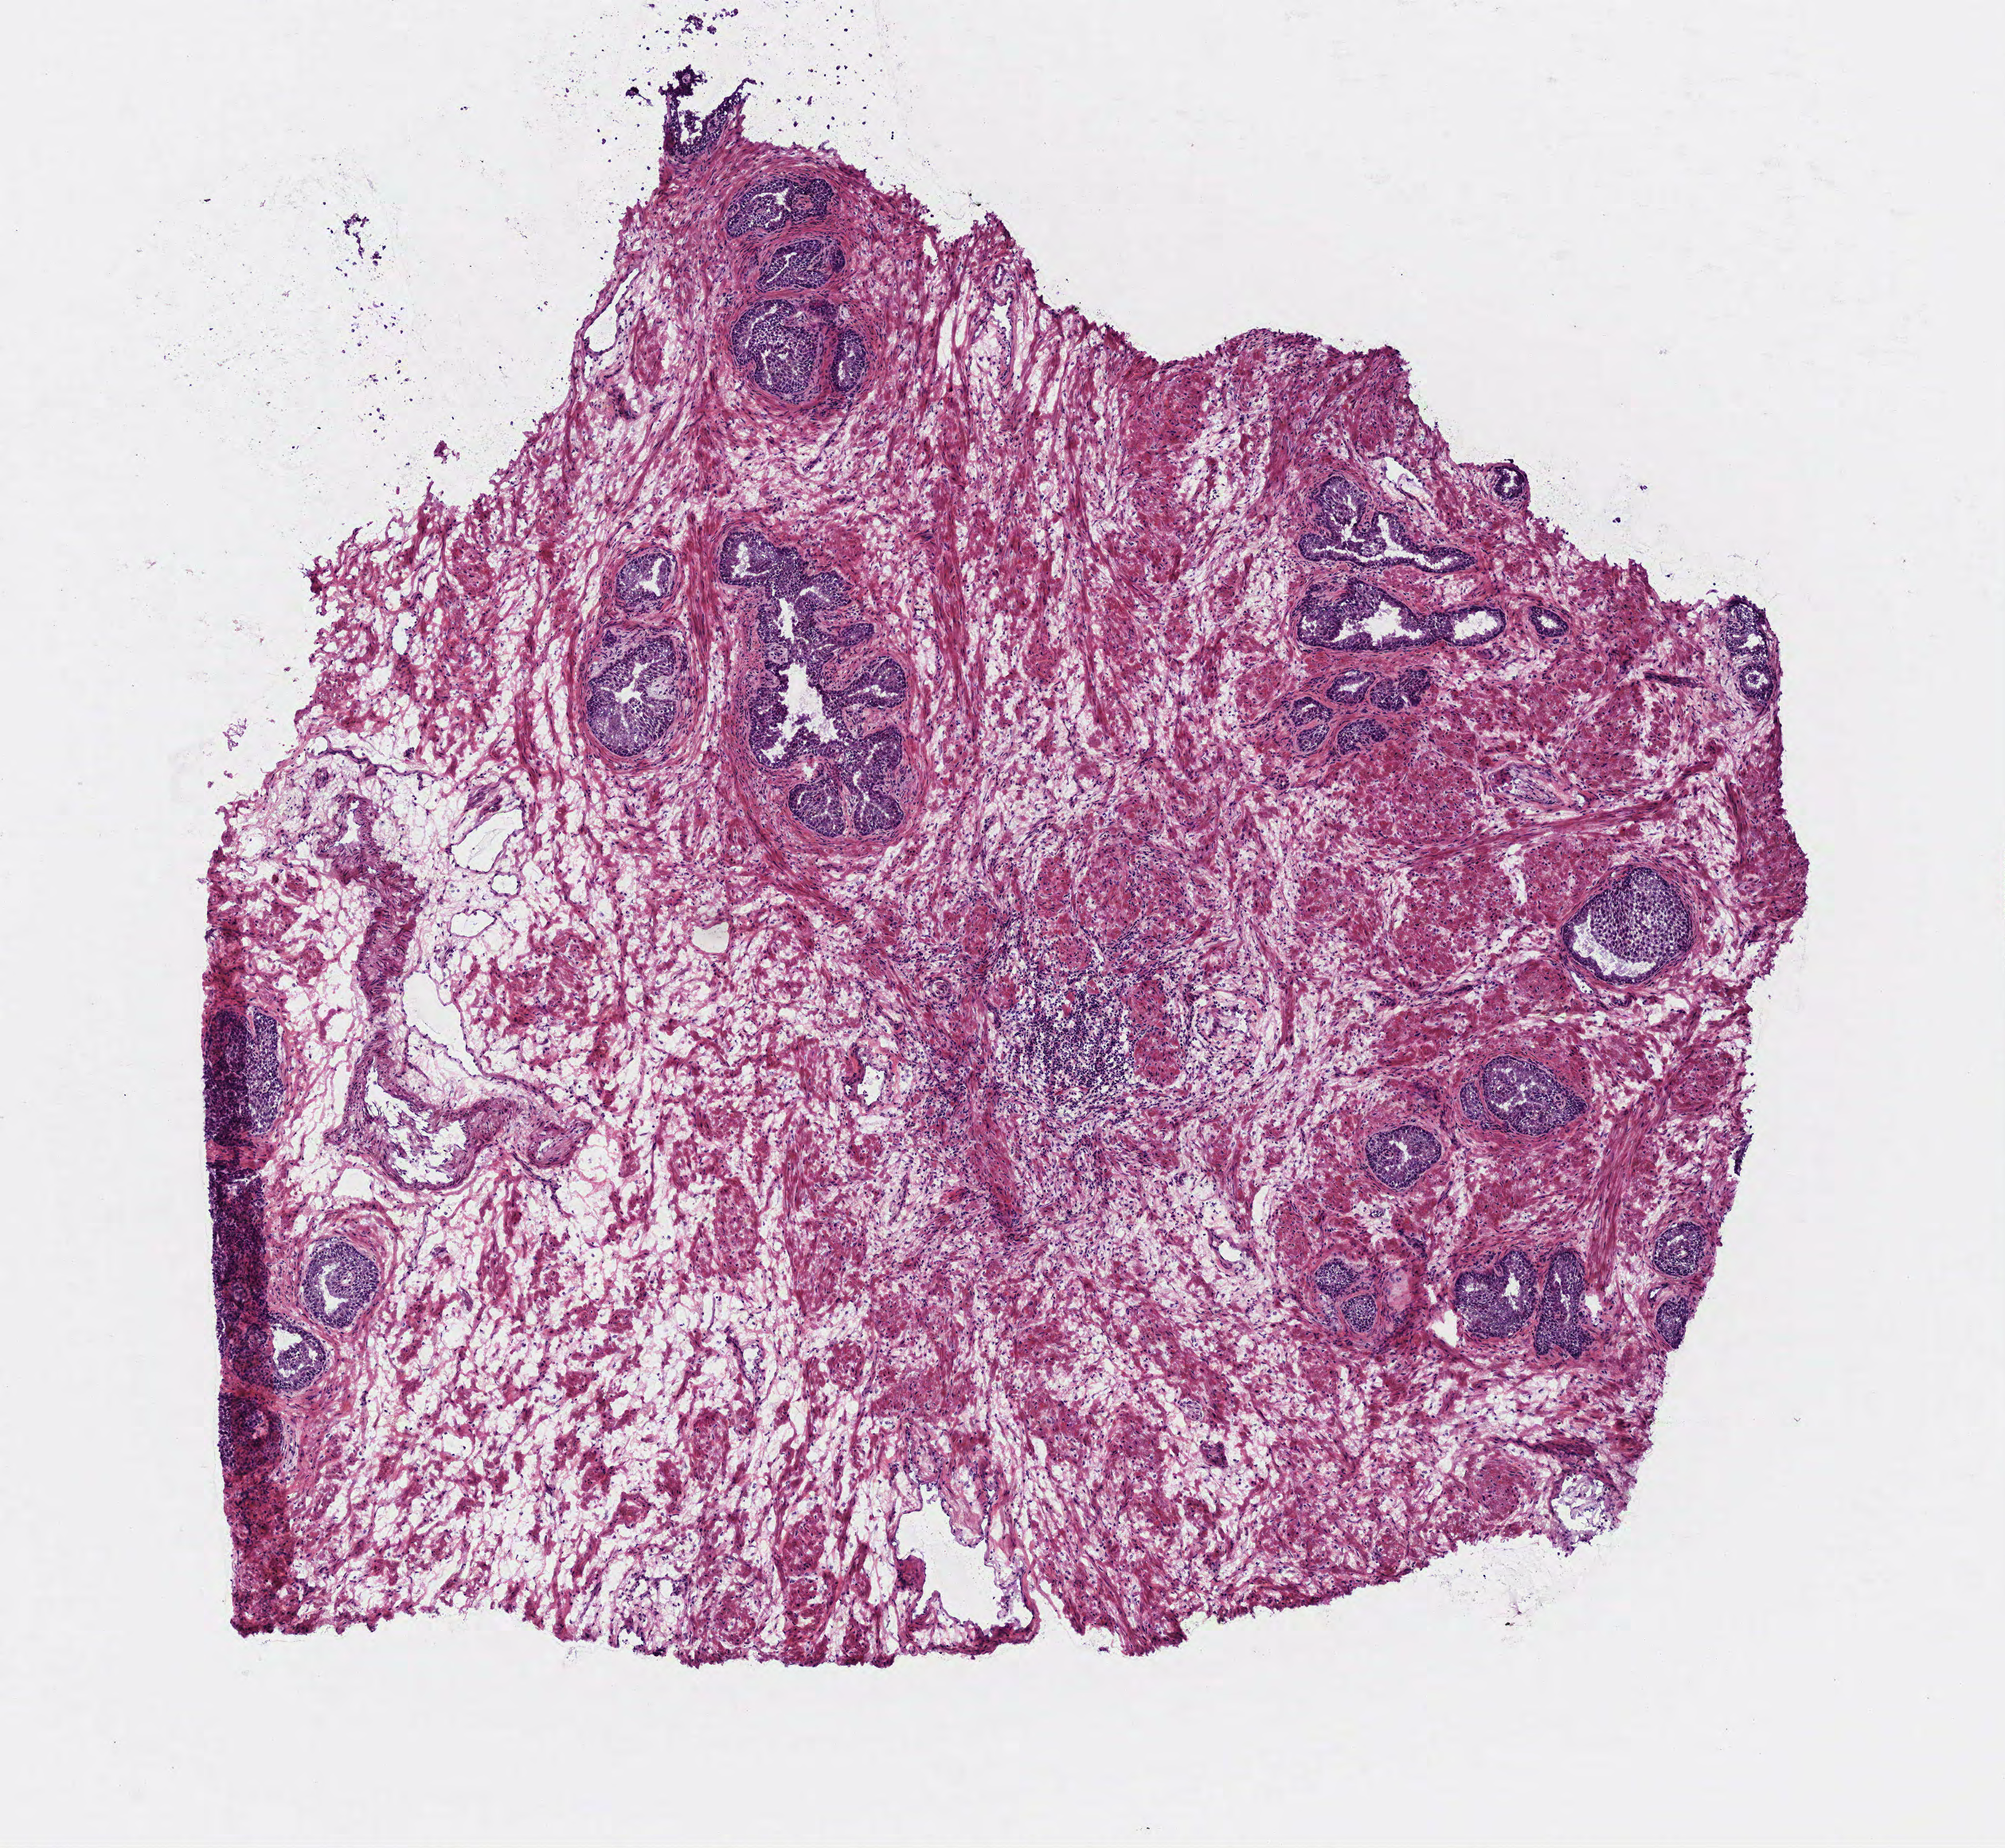
Digitized H&E-stained tissue section (whole slide) — a low-resolution overview of the entire scanned area, about 5.1 x 4.7 mm. Frozen section from the top of the tissue portion. Sample: solid tissue normal (non-tumour tissue), prostate. Male, age 57 years at initial diagnosis.
This section: solid tissue normal sample (biorepository sample class). Patient diagnosis: Acinar cell carcinoma (prostate gland).